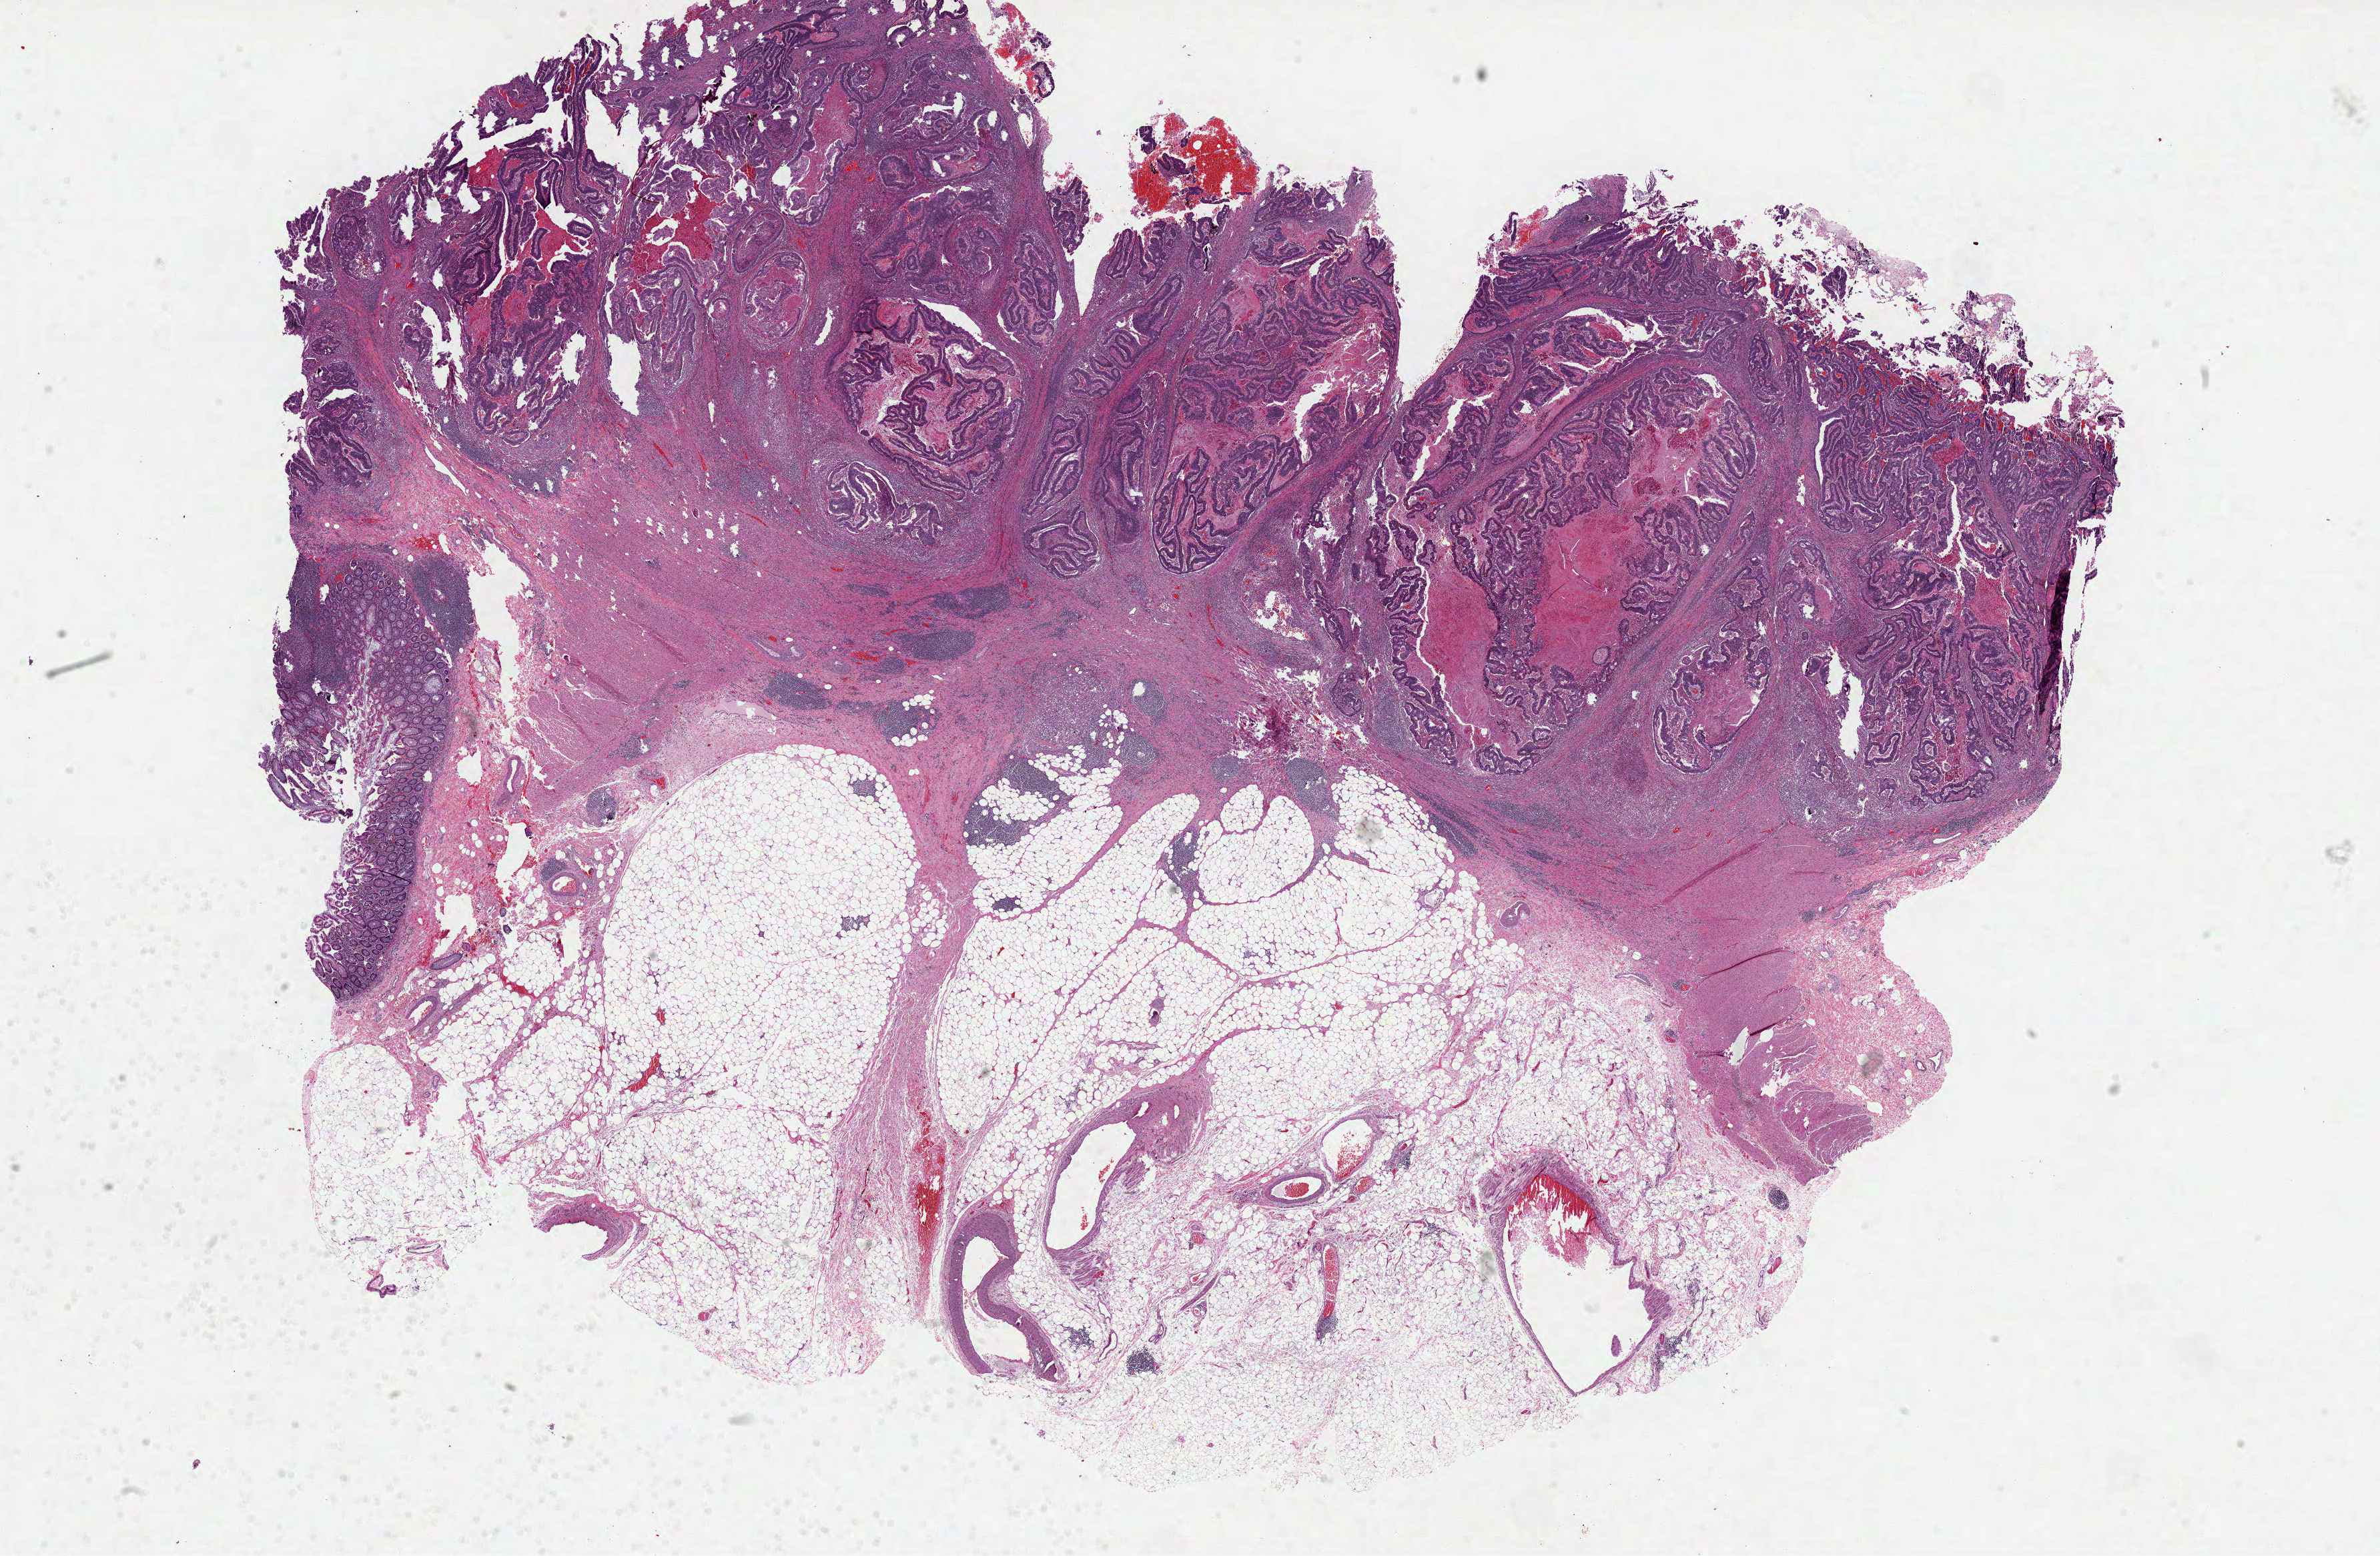
Whole-slide histology image, Hematoxylin and eosin (H&E) stained, whole scanned area (about 28.8 x 18.8 mm) shown as a low-resolution overview. Formalin-fixed paraffin-embedded (FFPE) diagnostic section. Colon, primary tumour sample. Patient: male, age at initial diagnosis 67 years.
• lymph nodes positive (case pathology): 0 of 19 examined
• pathologic diagnosis: Adenocarcinoma, NOS (cecum)
• AJCC pathologic stage: IIA